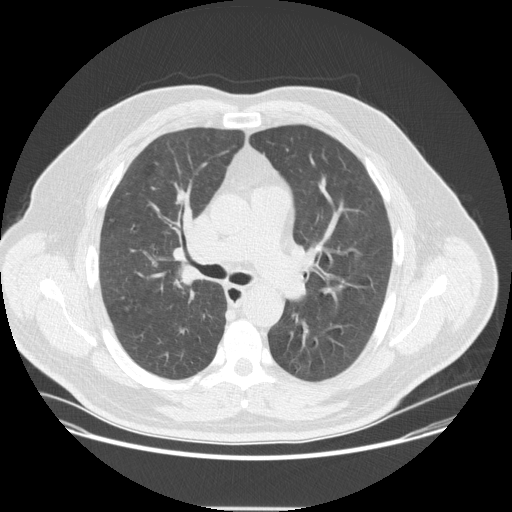
Low-dose screening chest CT, one axial slice. Reconstruction kernel STANDARD. 120 kVp. Lung window (W 1500 / L -600 HU). 2.5 mm slice thickness. 512 × 512 image matrix.
Annotated regions visible in this slice (manually delineated by an expert):
- lesion 1 (tumor, upper lobe of right lung): bounding box (x1, y1, x2, y2) in pixels: (178, 271, 199, 285)